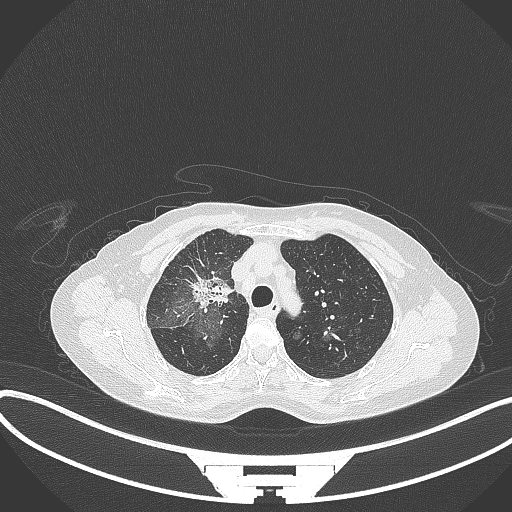
Chest CT, one axial slice; position 242 of 284 along the scan axis; reconstruction kernel B70f; lung window (W 1500 / L -600 HU); 512 × 512 image matrix, field of view 400 × 400 mm. Female patient, age 59 years. From the clinical record (not read from this slice): clinical TNM (as recorded): T3 N0 M0; histopathological grade: G1.
Structures marked on this image (rectangle marked by the reading radiologist):
- lung tumour (recorded histology: adenocarcinoma): box from (x=187, y=268) to (x=233, y=308) px